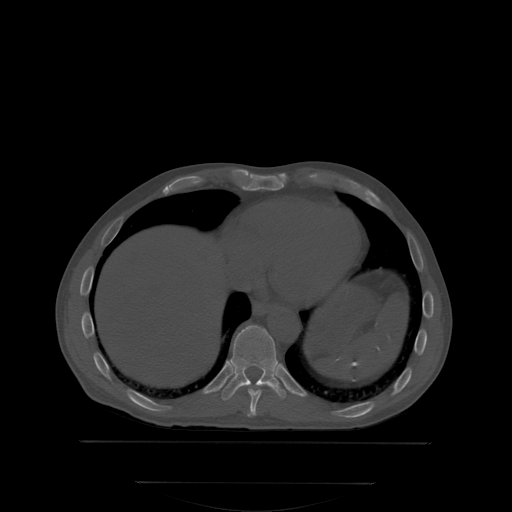
CT including the spine, one axial slice. Slice 197 of 350 in the series (ordered by position). Bone window (W 1800 / L 400 HU). 512 × 512 image matrix, field of view 500 × 500 mm. Male patient, age 58 years. From the clinical record (not read from this slice): primary cancer: prostate; vertebrae with lytic lesions (as recorded): L1.
Structures marked on this image (semi-automatically segmented with operator editing):
- T10 vertebra: bounding box <222,325,286,400> (left, top, right, bottom; pixels)
- T9 vertebra: <240,384,274,415>